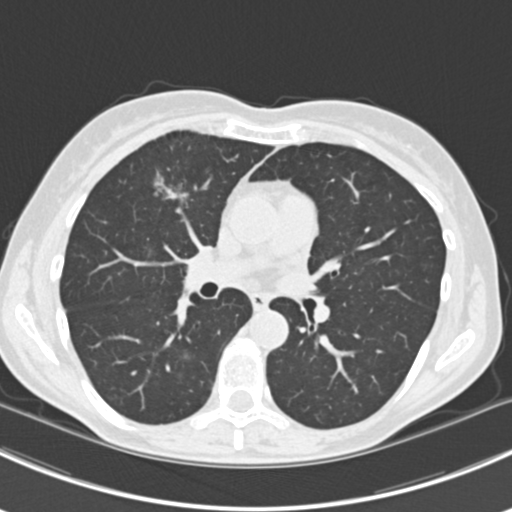
Chest CT (low-dose screening protocol), one axial image, first (baseline) screen, lung window (W 1500 / L -600 HU), standard (soft-tissue) reconstruction kernel (B30f), slice 84 of 224 in the series, 512 × 512 image matrix. Female participant, aged 63 years at enrolment. Current smoker at enrolment.
• Expert reader's lesion annotation, bounding box (x1, y1, x2, y2) in pixels: (144, 164, 203, 220).
• The screening reader recorded 10 non-calcified nodules or masses ≥4 mm on this exam (right lower lobe, right lower lobe, left lower lobe, left lower lobe, right middle lobe, right lower lobe, left lower lobe, left upper lobe, right upper lobe, left upper lobe); which of them this box marks is not recorded.
• Official screen result: positive, change unspecified: nodule(s) >= 4 mm or enlarging nodule(s), mass(es), or other non-specific abnormalities suspicious for lung cancer.